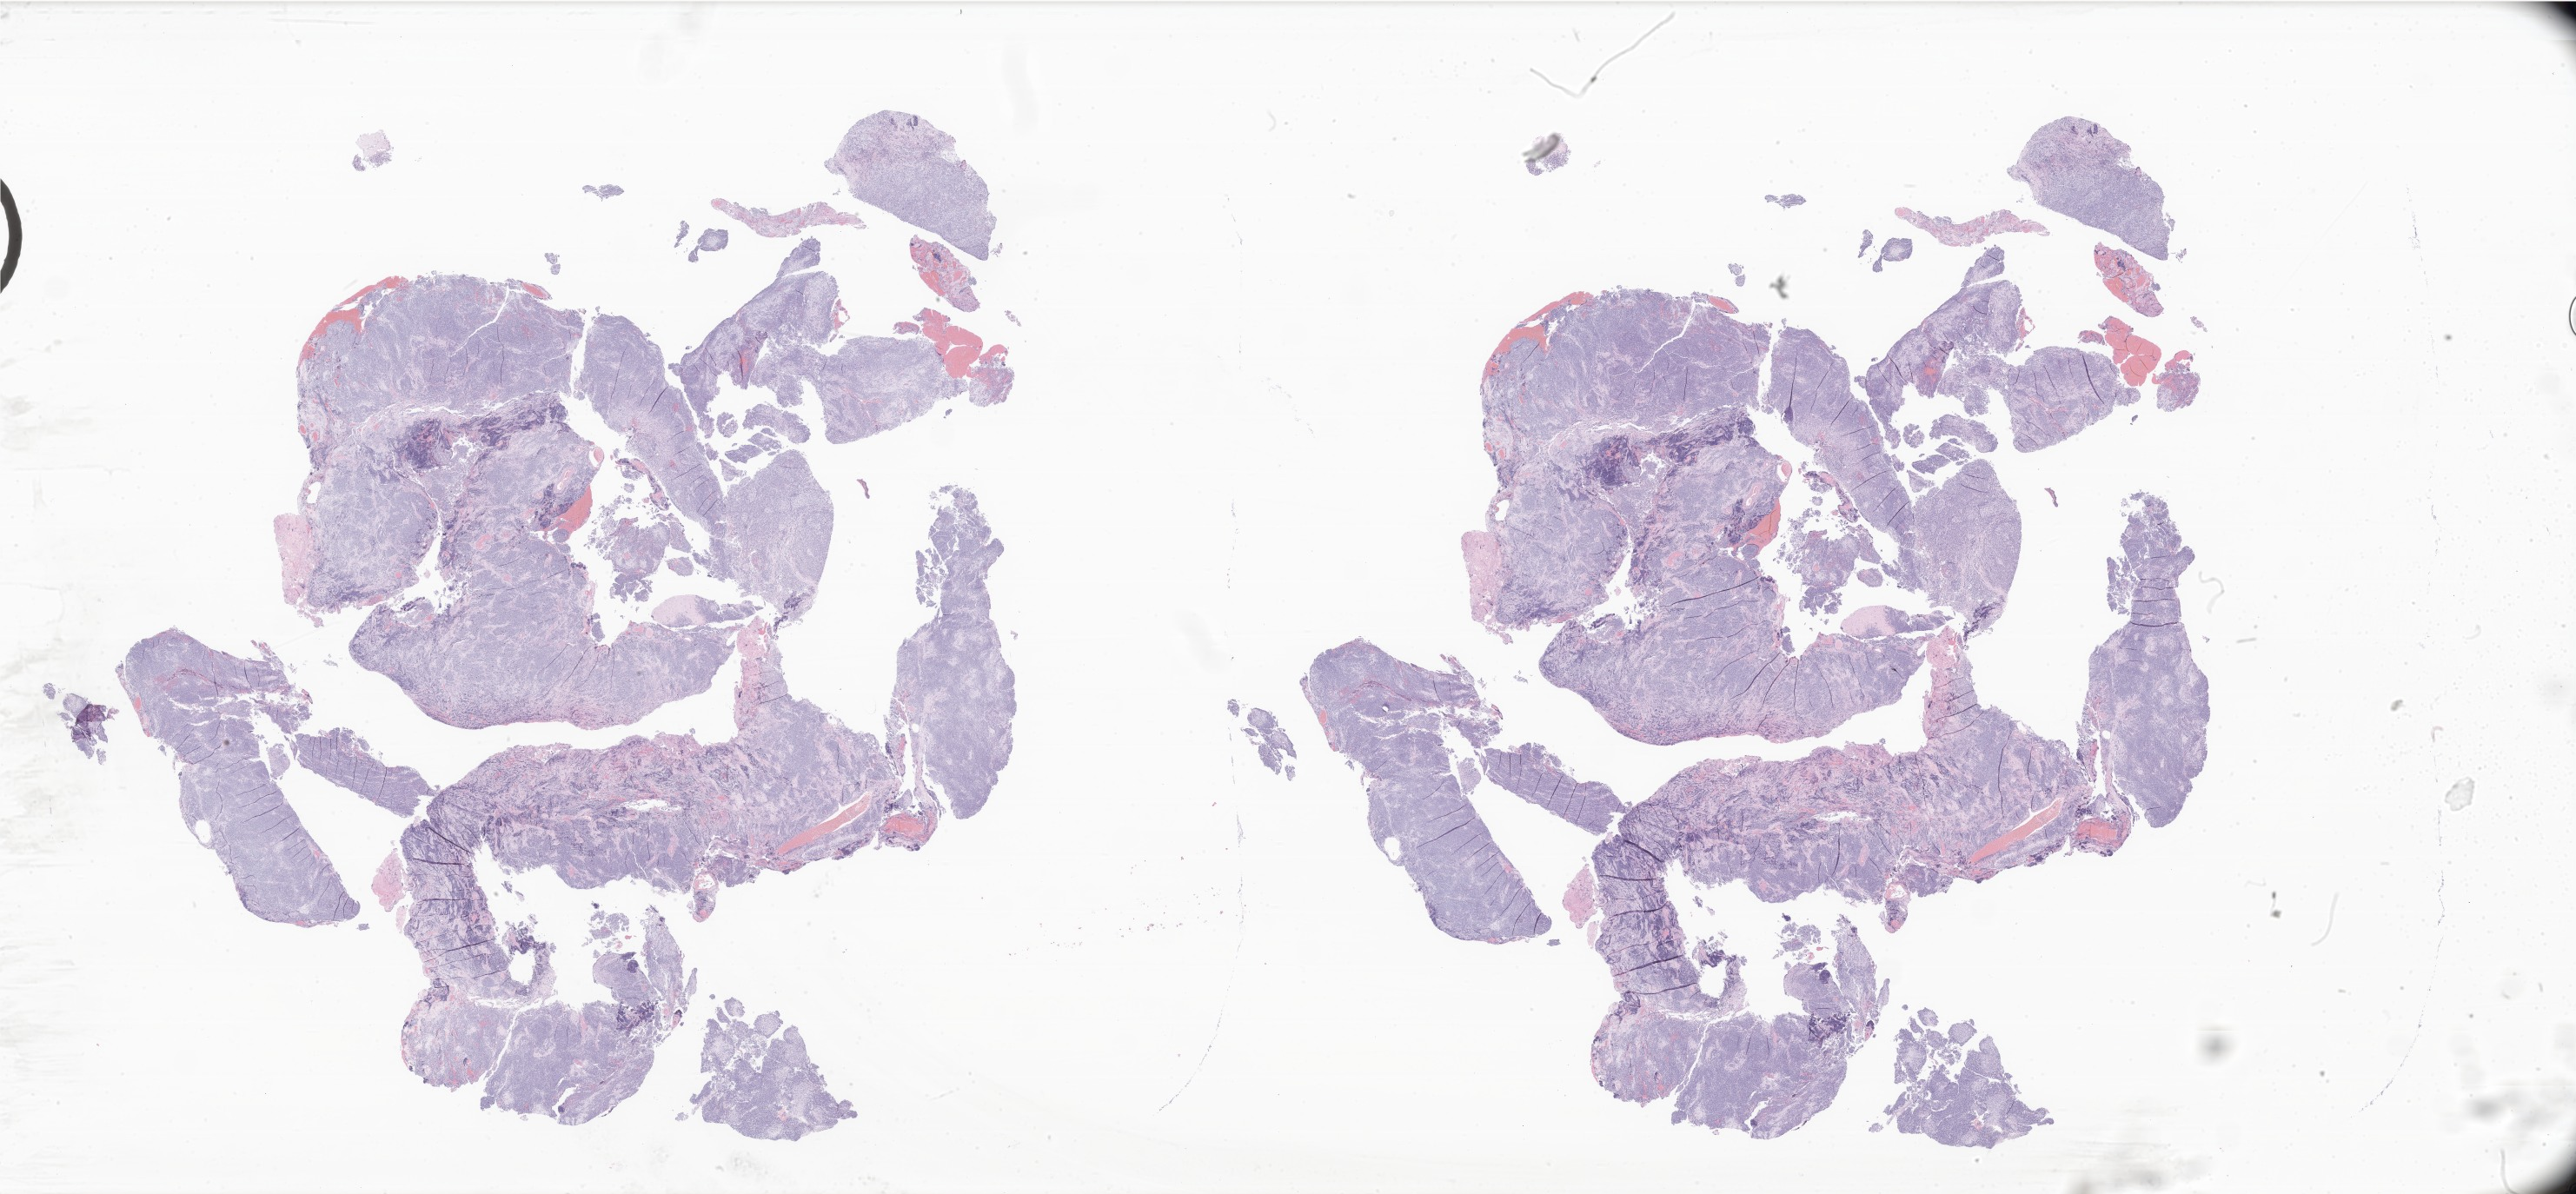
Haematoxylin and eosin whole-slide image of tumor tissue from the brain — whole scanned area (about 50.0 x 23.2 mm) shown as a low-resolution overview; formalin-fixed paraffin-embedded section. Patient male; age 160 months (13 years 4 months).
Diagnosis: Medulloblastoma, NOS.